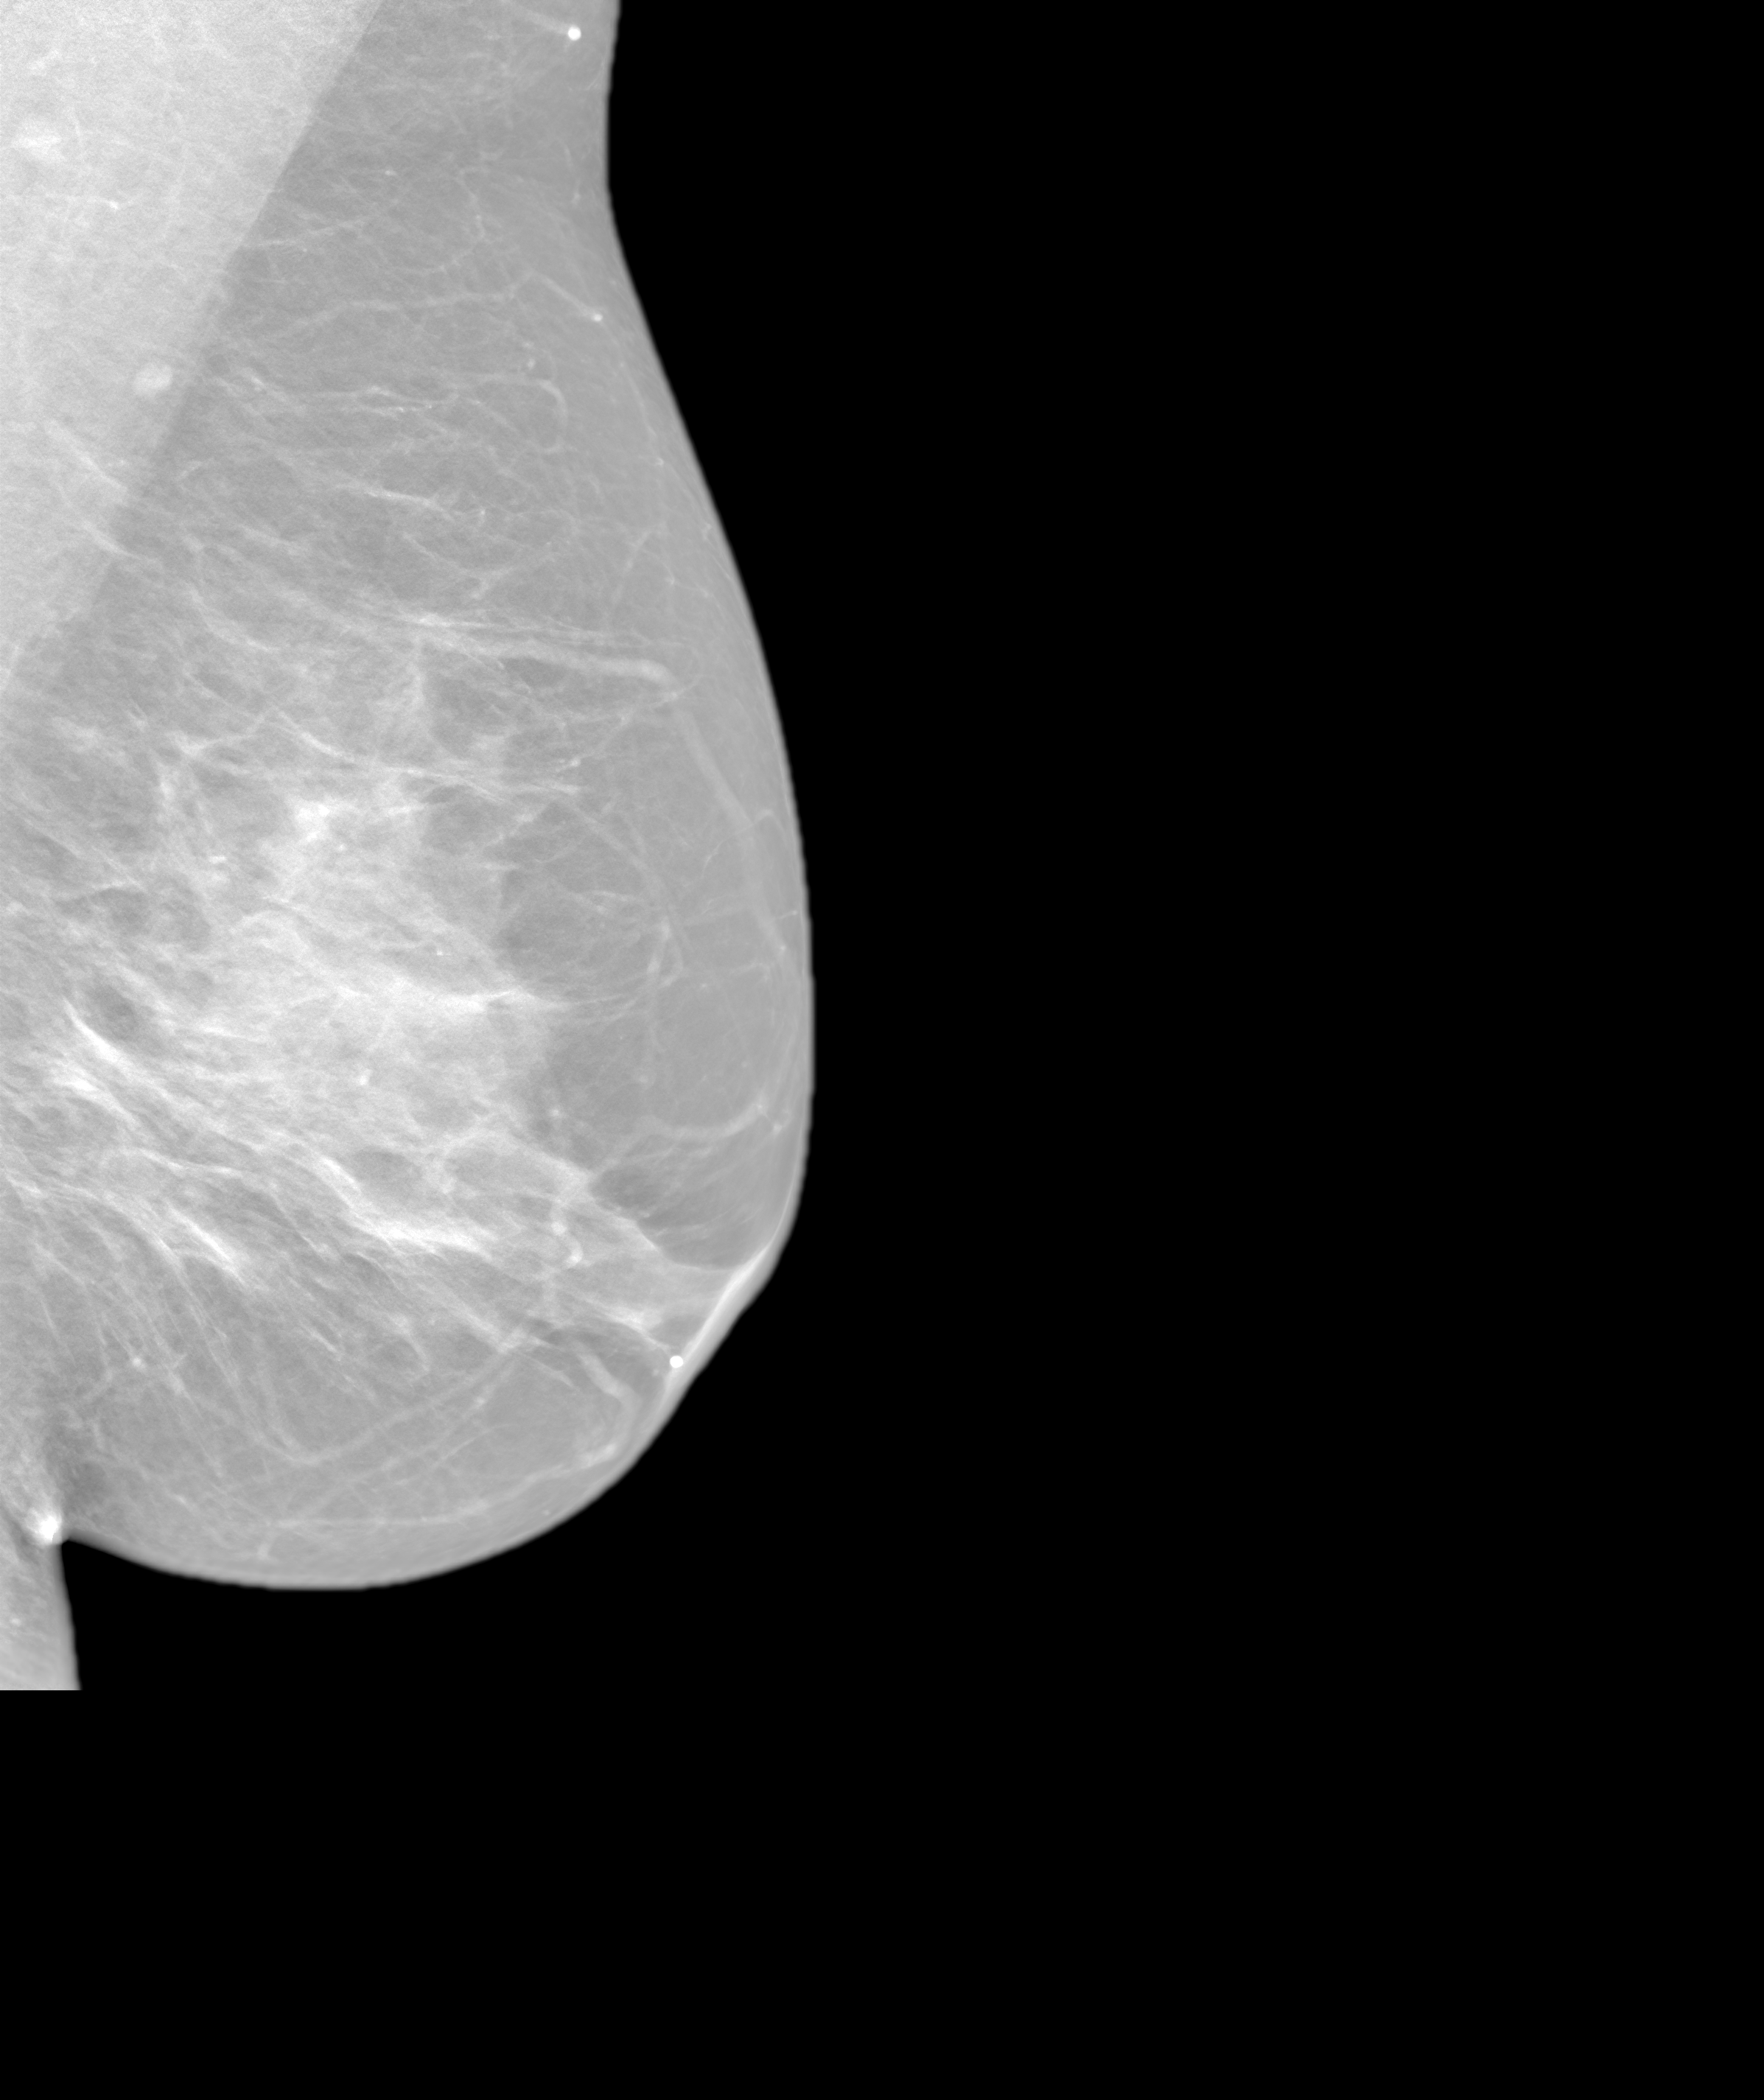
Annual screening mammography examination. Female patient, age 48 years.
Image type: synthesized 2-D view from tomosynthesis. Breast: left. Projection: medio-lateral oblique projection.